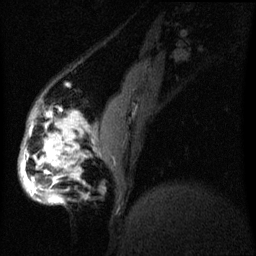
Breast MRI (dynamic contrast-enhanced), one sagittal slice; slice 15 of 60 in the series (ordered by position); dynamic contrast-enhanced series, image 2 of 3 at this slice position (ordered by acquisition); 1.5 T; TE 4.2 ms, TR 8 ms; 256 × 256 image matrix, field of view 200 × 200 mm. Patient: female, 50 years.
Annotated regions visible in this slice (semi-automatically segmented with operator editing):
- analysis volume of interest (the breast-tissue region the enhancement analysis was run in; not a lesion): bounding box <19,112,80,207> (left, top, right, bottom; pixels)
- tumour enhancement mask (voxels above the 70 % enhancement threshold inside the analysis volume of interest): <22,120,72,203>